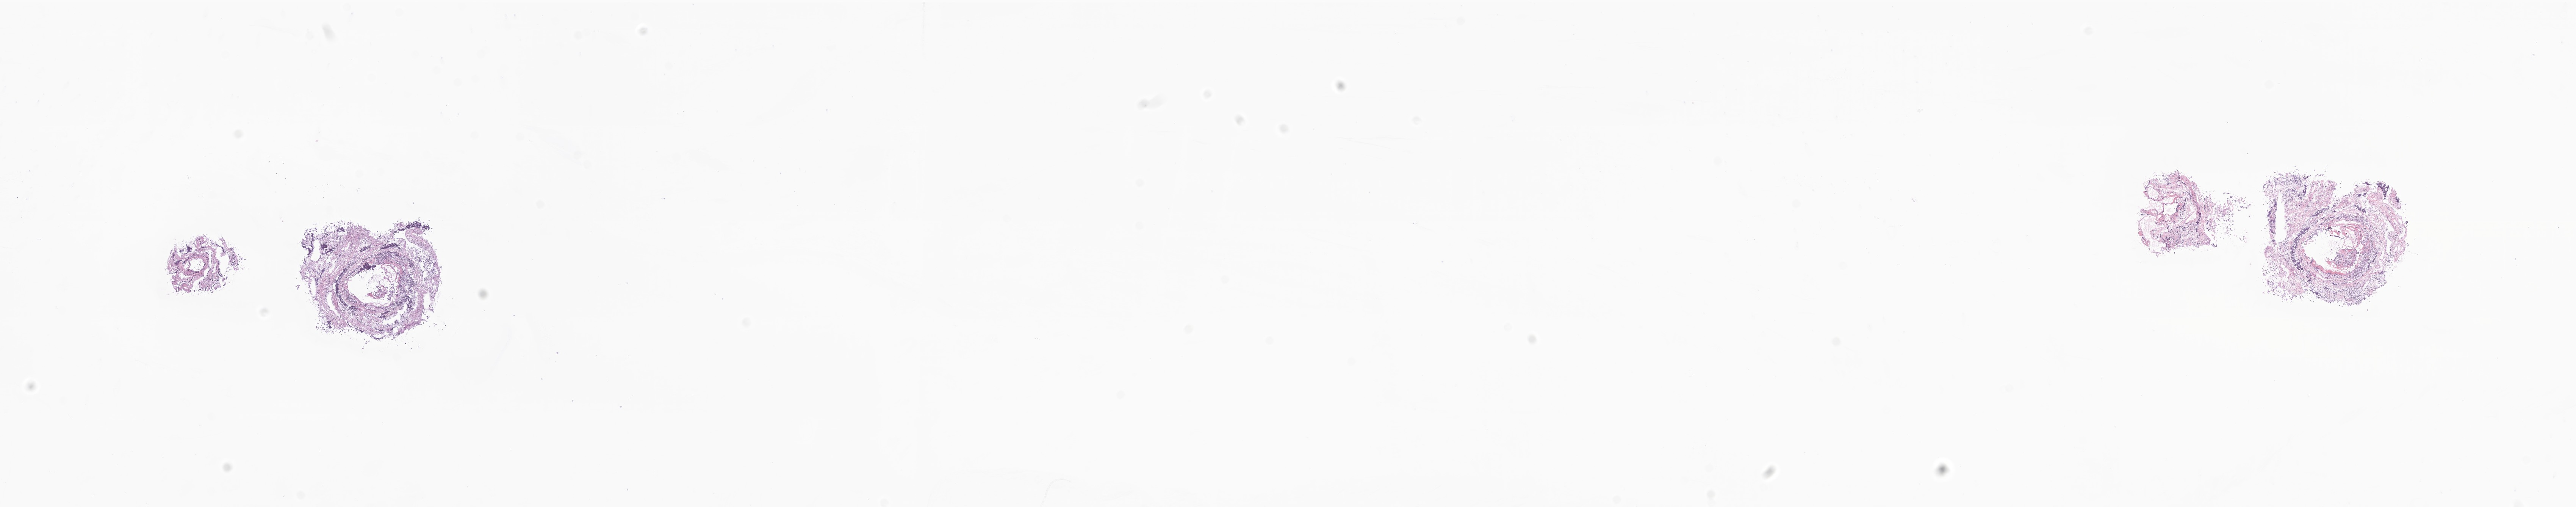
Haematoxylin and eosin whole-slide image of tumor tissue from the brain, whole scanned area (about 28.7 x 5.6 mm) shown as a low-resolution overview; frozen section. Female patient, age 79 months (6 years 7 months).
Diagnosis: Medulloblastoma, NOS.